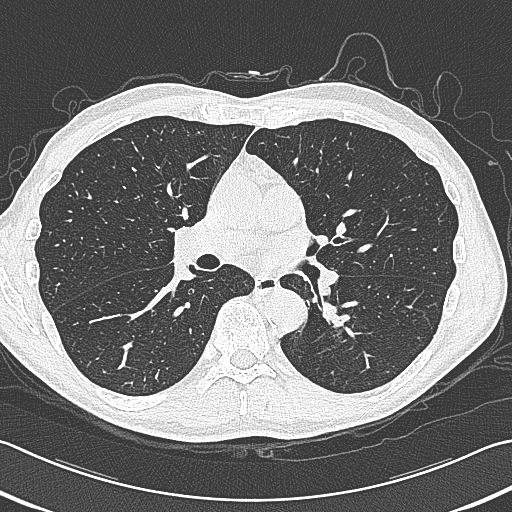
Low-dose screening chest CT, axial slice, baseline annual screen, lung window (W 1500 / L -600 HU), 1 mm slice thickness, slice 161 of 354 in the series. Male participant, aged 59 years at enrolment.
Expert-annotated lung lesion, box from (x=314, y=292) to (x=375, y=353) px. Screening reader's record for this exam (one nodule recorded; not confirmed to be the boxed lesion): non-calcified nodule or mass ≥4 mm, left lower lobe, 15 × 15 mm, smooth margins, soft tissue attenuation. Later outcome: lung cancer diagnosed 17 days after this screen — squamous cell carcinoma, large cell, nonkeratinizing, NOS, left lower lobe, poorly differentiated (G3), stage IB (AJCC 6th edition), 31 mm at pathology.